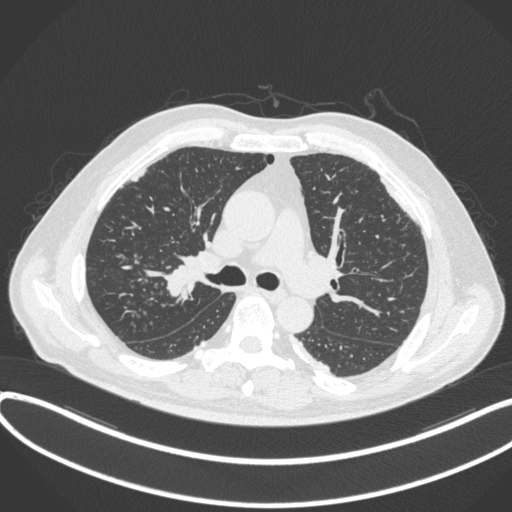
Chest CT, one axial slice; slice 266 of 455 in the series (ordered by position); reconstruction kernel B31f; 120 kVp; lung window (W 1500 / L -600 HU); 1 mm slice thickness; 512 × 512 image matrix, field of view 400 × 400 mm. Patient: male, 58 years. Case-level facts recorded for this patient, not image findings: clinical TNM (as recorded): T1c N0 M0.
Outlined on this slice (rectangle marked by the reading radiologist):
- lung tumour (recorded histology: squamous cell carcinoma): bounding box [x1, y1, x2, y2] px = [162, 260, 205, 308]